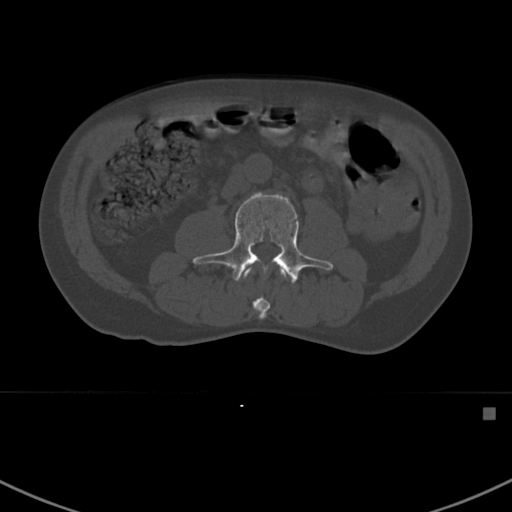
CT including the spine, one axial slice; slice 267 of 412 in the series (ordered by position); reconstruction kernel Br40s; 120 kVp; bone window (W 1800 / L 400 HU); 1.5 mm slice thickness; 512 × 512 image matrix, field of view 358 × 358 mm. Male patient, age 59 years. From the clinical record (not read from this slice): primary cancer: prostate.
Outlined on this slice (semi-automatic segmentation, software-assisted and operator-edited):
- L2 vertebra: bounding box [x1, y1, x2, y2] px = [243, 268, 288, 319]
- L3 vertebra: [191, 192, 334, 283]